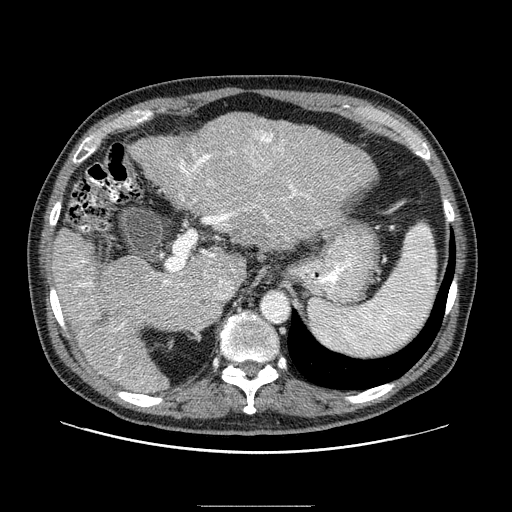
Contrast-enhanced abdominal CT (liver protocol), one axial slice. 100 kVp. One of 2 acquisitions stored at this slice position. Soft-tissue window (W 400 / L 40 HU). 2.5 mm slice thickness. 512 × 512 image matrix. From the clinical record (not read from this slice): diagnosis: hepatocellular carcinoma (patient treated with transarterial chemoembolisation; whether this scan precedes or follows treatment is not stated here); TNM stage (as recorded): Stage-II; Child-Pugh class: A; tumour differentiation: well differentiated; tumour nodularity: multinodular.
Annotated regions visible in this slice (semi-automatically segmented with operator editing):
- liver parenchyma outside the tumour (the mass and vessels are separate outlines, so this box may not span the whole liver): bounding box <52,114,376,390> (left, top, right, bottom; pixels)
- mass: <239,130,285,174>
- liver vessels: <75,140,352,367>